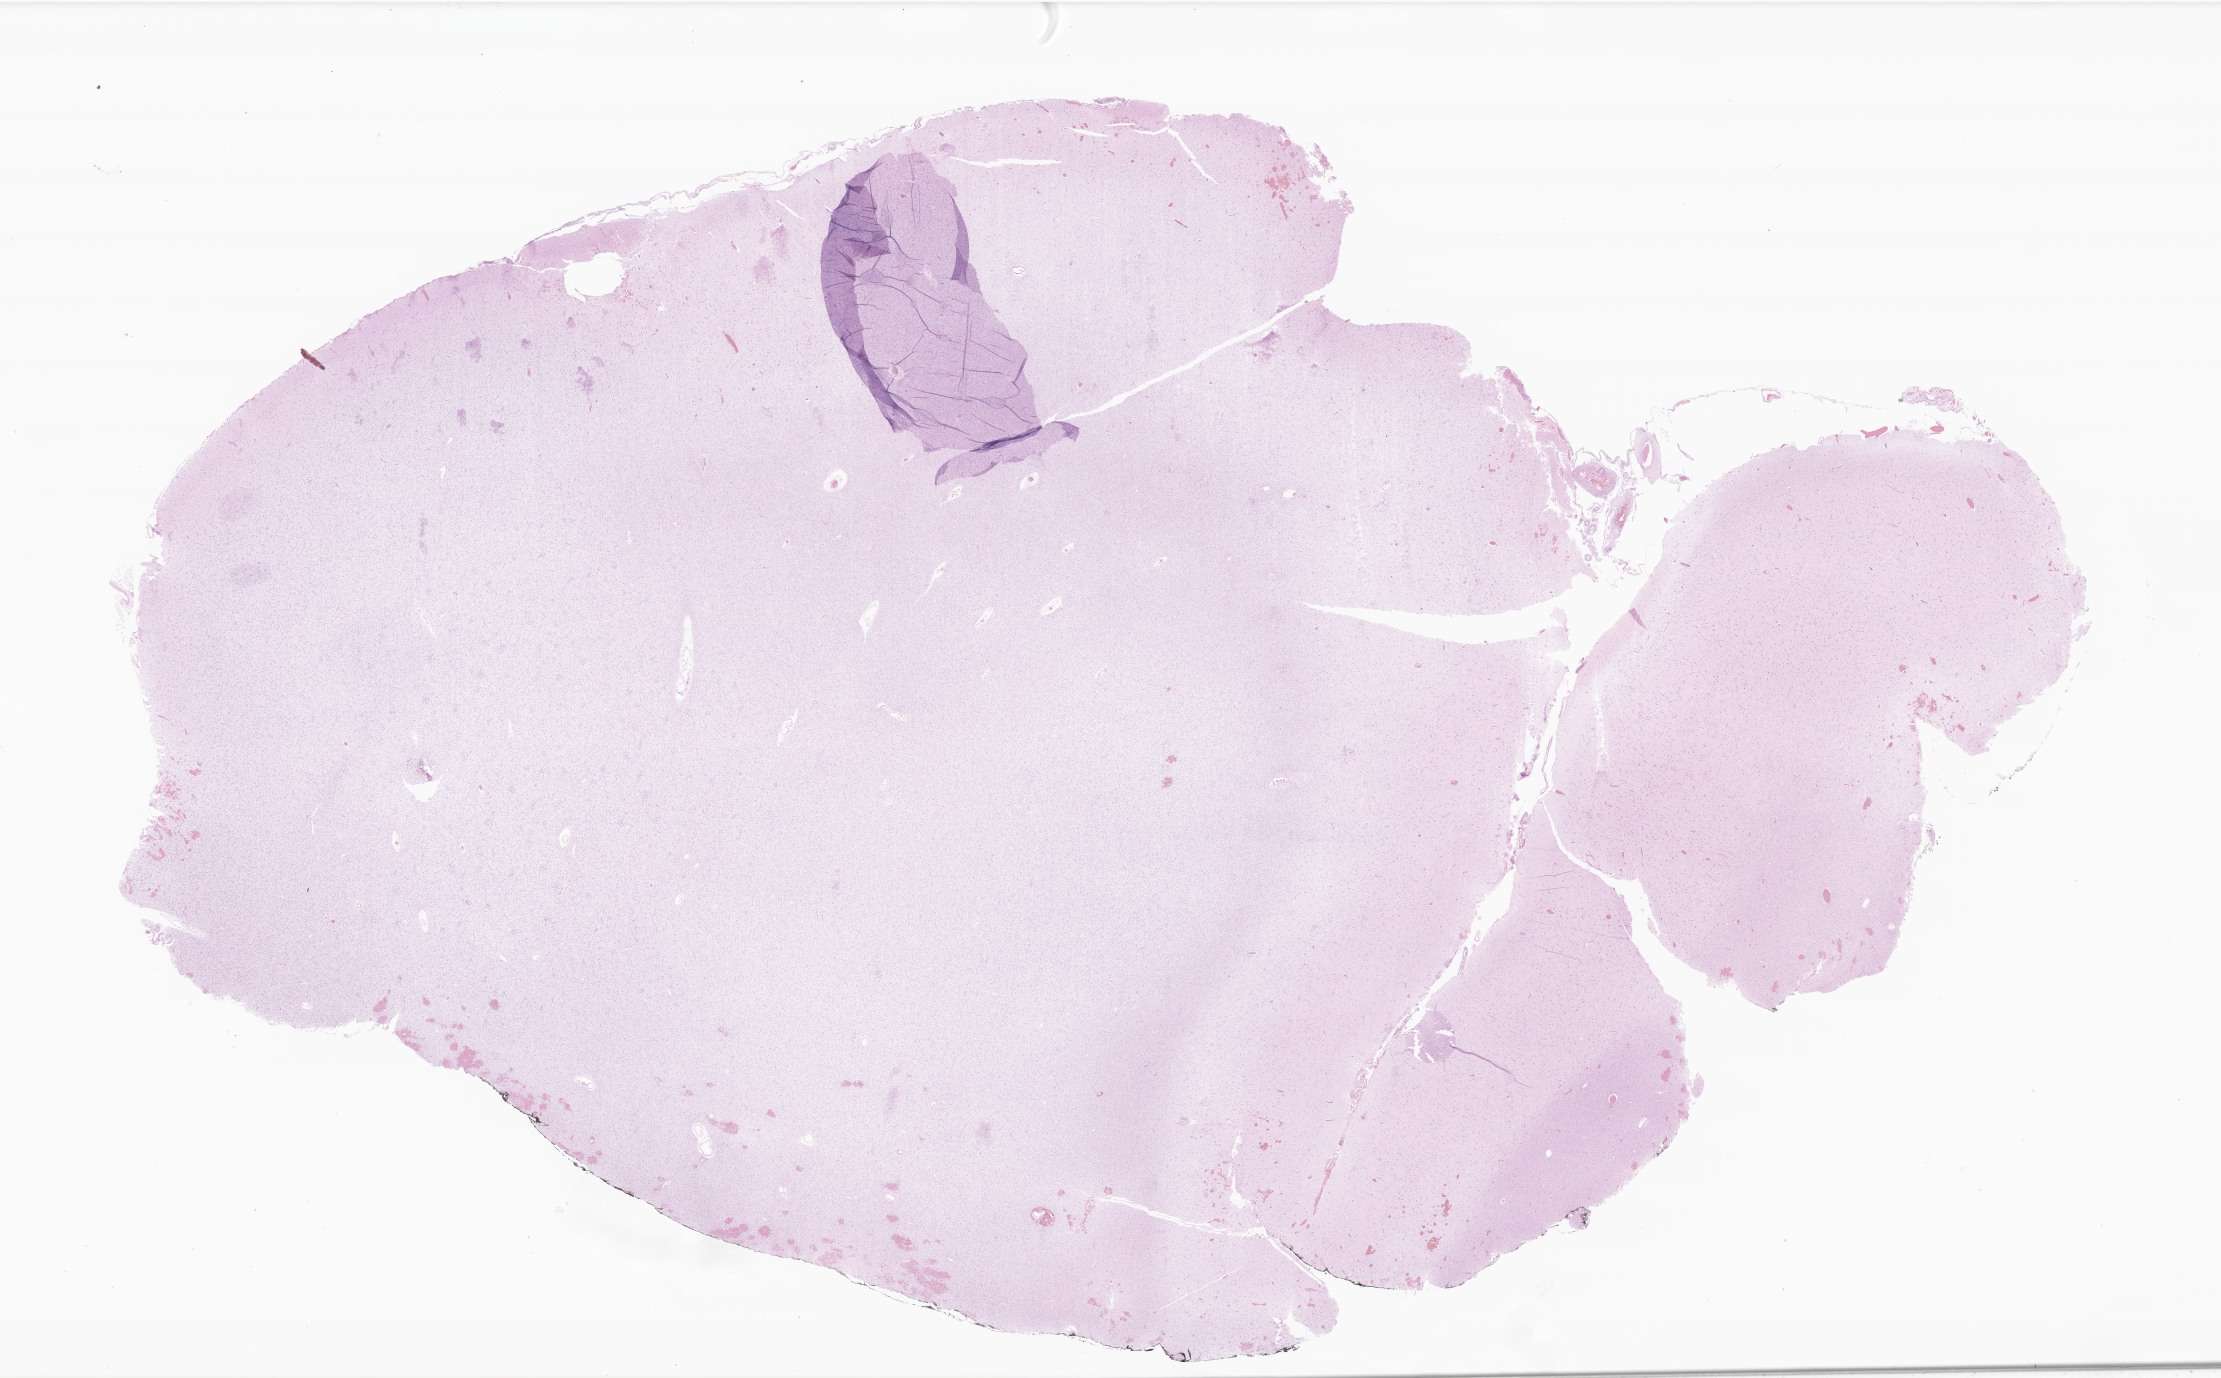
Hematoxylin and eosin (H&E) whole-slide image of tumor tissue from the brain, shown as a low-resolution overview of the whole scanned area (about 37.5 x 23.2 mm); formalin-fixed paraffin-embedded section. Female patient, age 315 months (26 years 3 months).
Recorded diagnosis: Astrocytoma, NOS.